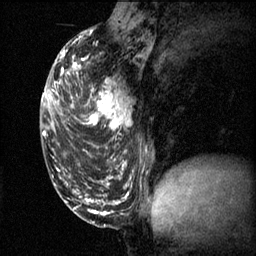
Breast MRI (dynamic contrast-enhanced), one sagittal slice; position 25 of 60 along the scan axis; 3 images stored at this slice position (order not interpretable as contrast timing); 1.5 T; TE 4.2 ms, TR 11.1 ms; 2 mm slice thickness; 256 × 256 image matrix, field of view 180 × 180 mm. Patient: female, 50 years.
Structures marked on this image (semi-automatically segmented with operator editing):
- analysis volume of interest (the breast-tissue region the enhancement analysis was run in; not a lesion): box from (x=68, y=68) to (x=139, y=141) px
- tumour enhancement mask (voxels above the 70 % enhancement threshold inside the analysis volume of interest): (x=68, y=68)–(x=133, y=131)